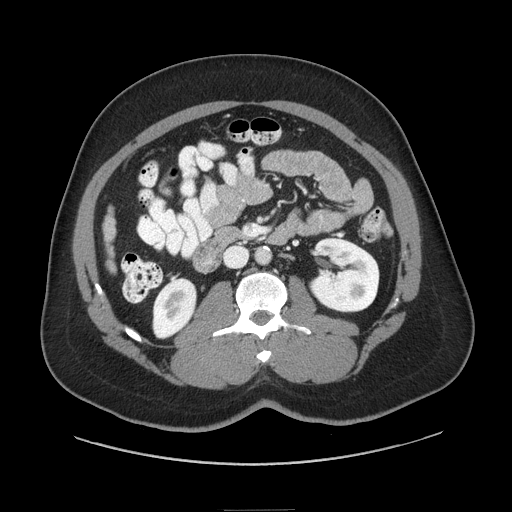
Contrast-enhanced abdominal CT (liver protocol), one axial slice. Position 16 of 87 along the scan axis. Soft-tissue window (W 400 / L 40 HU). 2.5 mm slice thickness. 512 × 512 image matrix, field of view 440 × 440 mm. From the clinical record (not read from this slice): diagnosis: hepatocellular carcinoma (patient treated with transarterial chemoembolisation; whether this scan precedes or follows treatment is not stated here); TNM stage (as recorded): Stage-II; Child-Pugh class: A; tumour differentiation: moderately differentiated; tumour nodularity: uninodular.
Structures marked on this image (semi-automatically segmented with operator editing):
- liver parenchyma outside the tumour (the mass and vessels are separate outlines, so this box may not span the whole liver): bounding box [x1, y1, x2, y2] px = [102, 212, 114, 272]